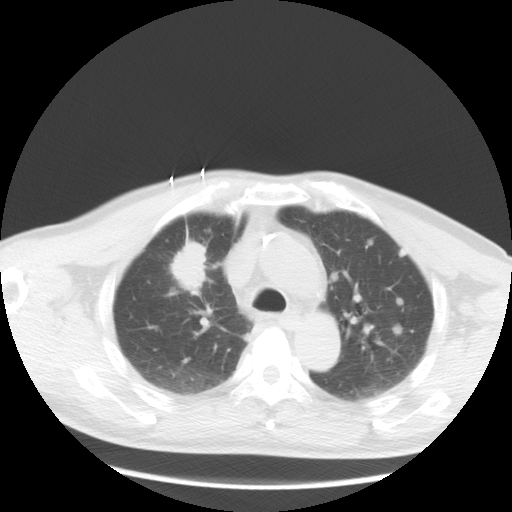
Chest CT, one axial slice; position 21 of 36 along the scan axis; reconstruction kernel STANDARD; 120 kVp; lung window (W 1500 / L -600 HU); 5 mm slice thickness; 512 × 512 image matrix, field of view 369 × 369 mm. Patient: male, 57 years. From the clinical record (not read from this slice): clinical TNM (as recorded): T2 N3 M1a.
Annotated regions visible in this slice (bounding box drawn by a radiologist):
- lung tumour (recorded histology: adenocarcinoma): bounding box [x1, y1, x2, y2] px = [166, 236, 208, 299]